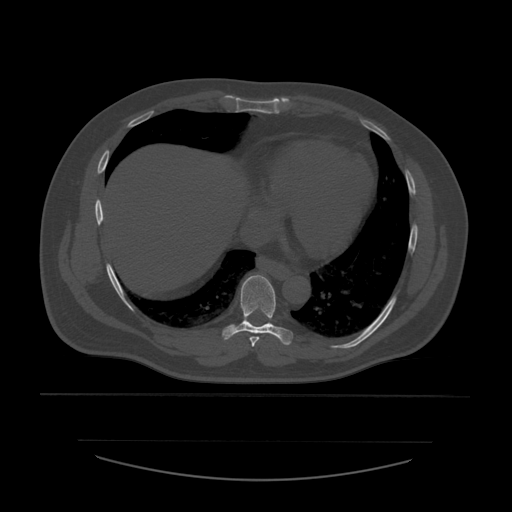
CT including the spine, one axial slice; slice 339 of 532 in the series (ordered by position); bone window (W 1800 / L 400 HU); 1.25 mm slice thickness; 512 × 512 image matrix, field of view 441 × 441 mm. Patient age 44 years. Case-level facts recorded for this patient, not image findings: primary cancer: soft tissue sarcoma.
Annotated regions visible in this slice (semi-automatic segmentation, software-assisted and operator-edited):
- T7 vertebra: bounding box <249,337,260,347> (left, top, right, bottom; pixels)
- T8 vertebra: <222,275,293,346>